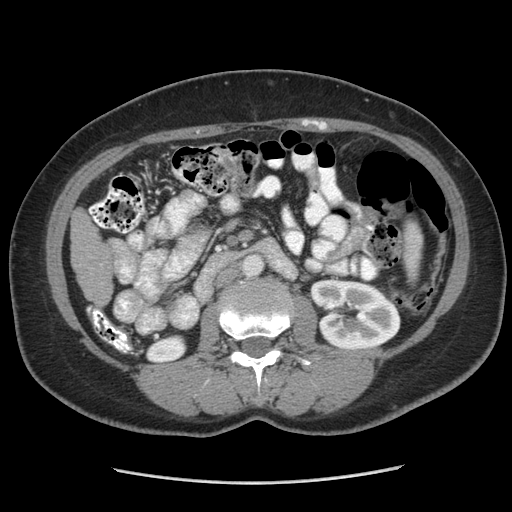
Contrast-enhanced abdominal CT (liver protocol), one axial slice. Reconstruction kernel STANDARD. 140 kVp. Soft-tissue window (W 400 / L 40 HU). 2.5 mm slice thickness. 512 × 512 image matrix, field of view 360 × 360 mm. Case-level facts recorded for this patient, not image findings: diagnosis: hepatocellular carcinoma (patient treated with transarterial chemoembolisation; whether this scan precedes or follows treatment is not stated here); TNM stage (as recorded): Stage-I; Child-Pugh class: A; tumour nodularity: uninodular.
Outlined on this slice (semi-automatically segmented with operator editing):
- liver parenchyma outside the tumour (the mass and vessels are separate outlines, so this box may not span the whole liver): box from (x=70, y=208) to (x=112, y=300) px